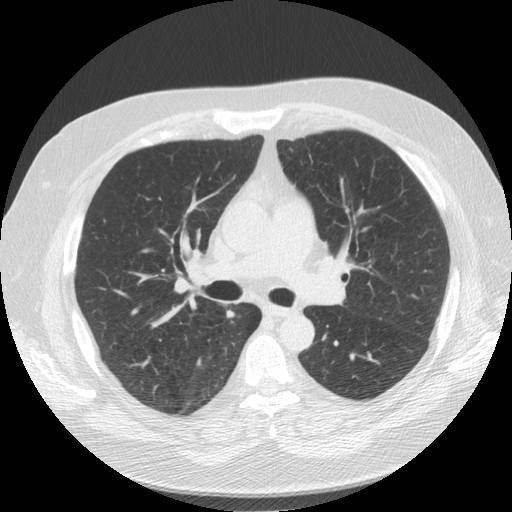
Low-dose screening chest CT, one axial slice. Position 88 of 136 along the scan axis. Reconstruction kernel STANDARD. 120 kVp. Lung window (W 1500 / L -600 HU). 512 × 512 image matrix, field of view 360 × 360 mm.
Structures marked on this image (manually delineated by an expert):
- lesion 1 (tumor, upper lobe of right lung): bounding box <226,309,236,319> (left, top, right, bottom; pixels)